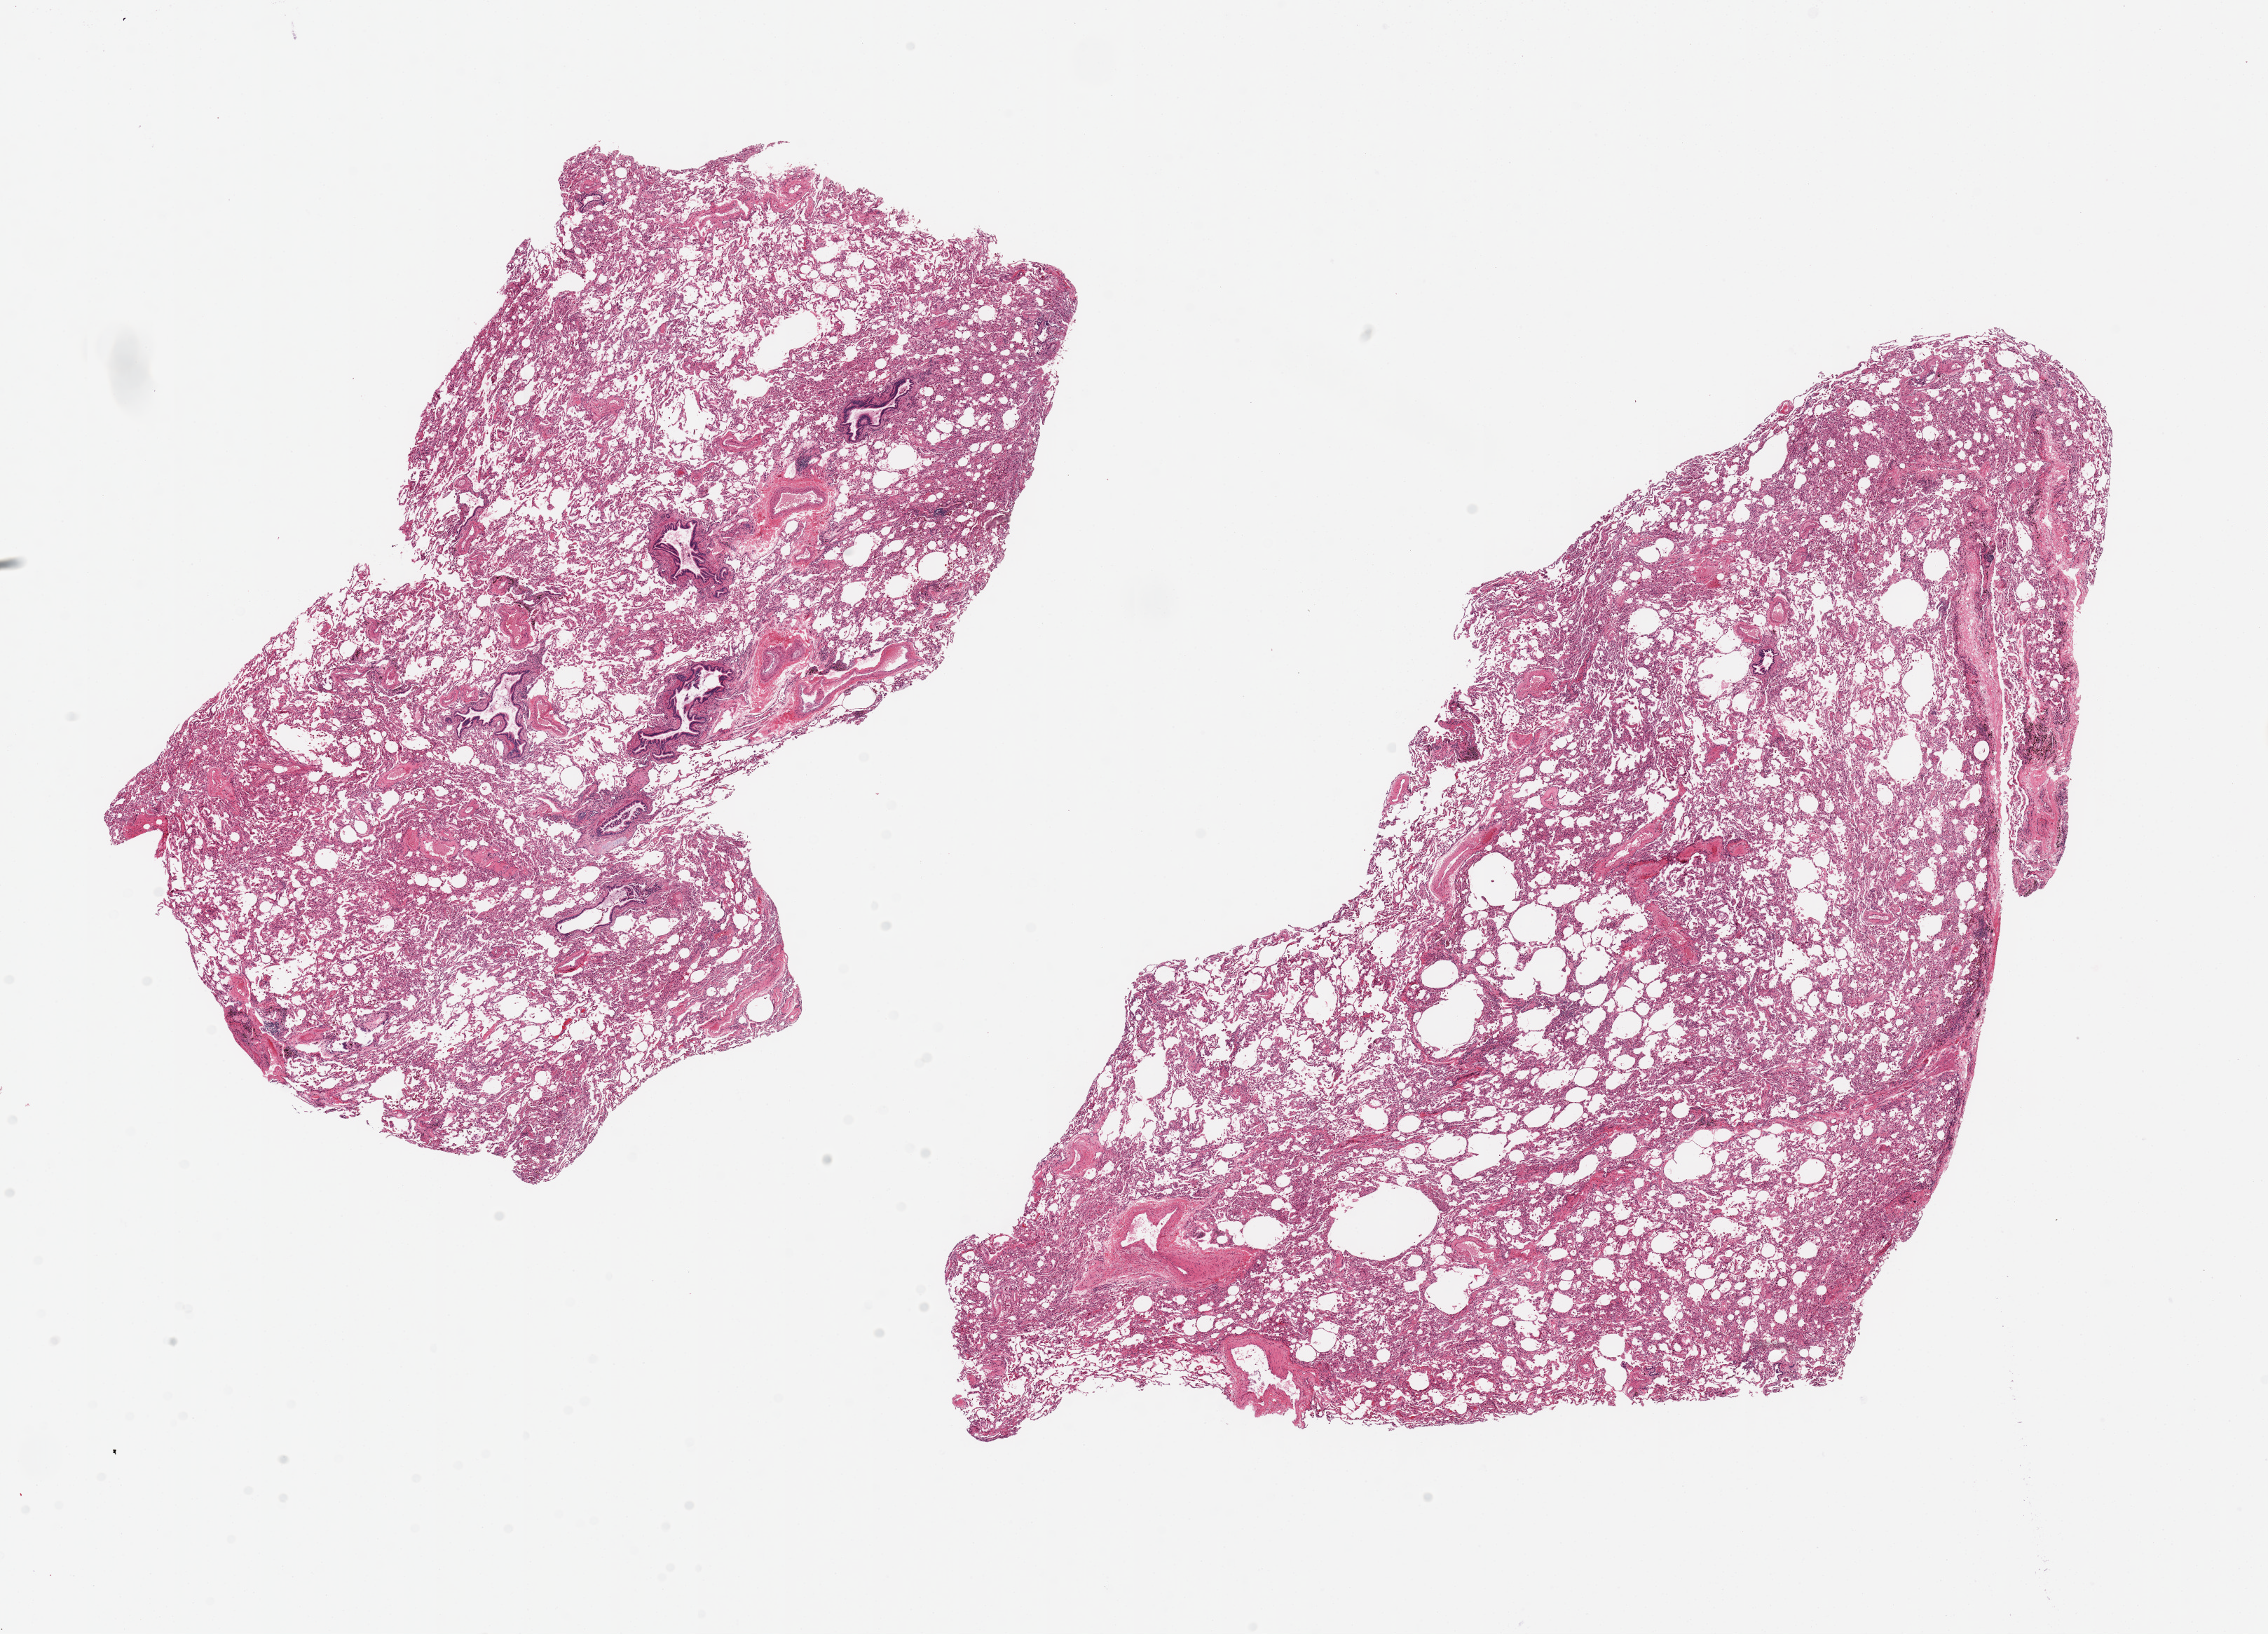
Haematoxylin and eosin whole-slide image — a low-resolution overview of the entire scanned area, about 25.6 x 18.4 mm. PAXgene-fixed, paraffin-embedded tissue. Target tissue: lung. Donor tissue sample. Donor sex: male.
Reviewer comment on this tissue sample: 2 pieces, 12x8 & 13x13mm; well -preserved bronchioles present; Emphysematous changes noted.